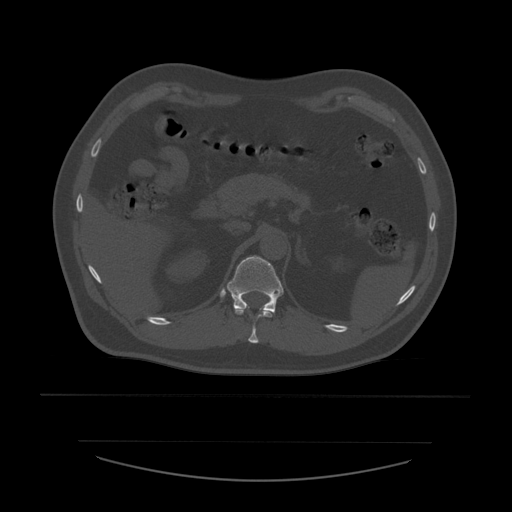
CT including the spine, one axial slice. Slice 260 of 532 in the series (ordered by position). Reconstruction kernel STANDARD. Bone window (W 1800 / L 400 HU). 1.25 mm slice thickness. 512 × 512 image matrix, field of view 441 × 441 mm. Patient age 44 years. Case-level facts recorded for this patient, not image findings: primary cancer: soft tissue sarcoma.
Annotated regions visible in this slice (semi-automatic segmentation, software-assisted and operator-edited):
- T11 vertebra: box from (x=235, y=309) to (x=275, y=344) px
- T12 vertebra: (x=227, y=256)–(x=284, y=312)